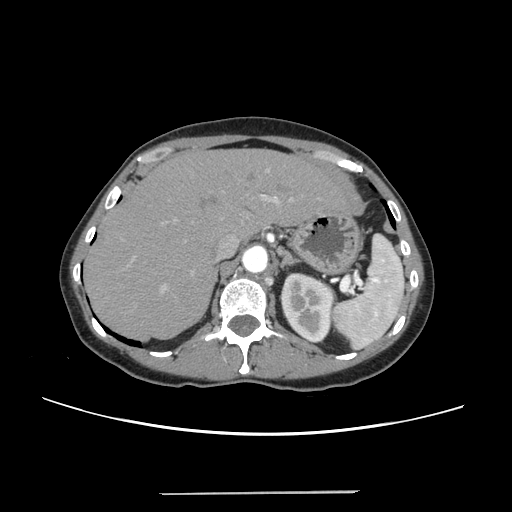
Contrast-enhanced abdominal CT, one axial slice; position 178 of 240 along the scan axis; intravenous contrast given; soft-tissue window (W 400 / L 40 HU); 512 × 512 image matrix. Female patient, age 60 years. Case-level facts recorded for this patient, not image findings: diagnosis: colorectal cancer liver metastases, imaged before liver resection; multiple liver metastases: no; largest metastasis: 1.5 cm; disease in both lobes: no.
Annotated regions visible in this slice (manually delineated by an expert):
- liver: box from (x=86, y=150) to (x=349, y=339) px
- planned liver remnant (the part of the liver to remain after resection): (x=86, y=150)–(x=348, y=339)
- portal vein (with intrahepatic branches): (x=133, y=170)–(x=294, y=293)